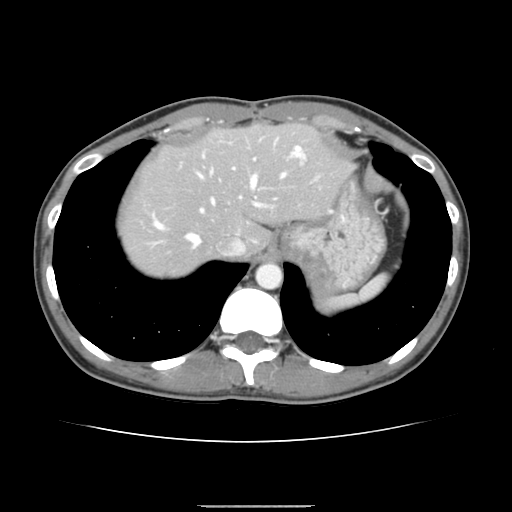
Contrast-enhanced abdominal CT, one axial slice. Slice 120 of 150 in the series (ordered by position). 120 kVp. Intravenous contrast given. Soft-tissue window (W 400 / L 40 HU). 2.5 mm slice thickness. 512 × 512 image matrix, field of view 324 × 324 mm. Female patient, age 32 years. Case-level facts recorded for this patient, not image findings: diagnosis: colorectal cancer liver metastases, imaged before liver resection; multiple liver metastases: yes; largest metastasis: 0.7 cm.
Structures marked on this image (outlined manually by an expert reader):
- hepatic veins: bounding box (x1, y1, x2, y2) in pixels: (154, 151, 295, 249)
- liver: (119, 124, 350, 277)
- planned liver remnant (the part of the liver to remain after resection): (120, 125, 351, 259)
- portal vein (with intrahepatic branches): (200, 146, 305, 212)